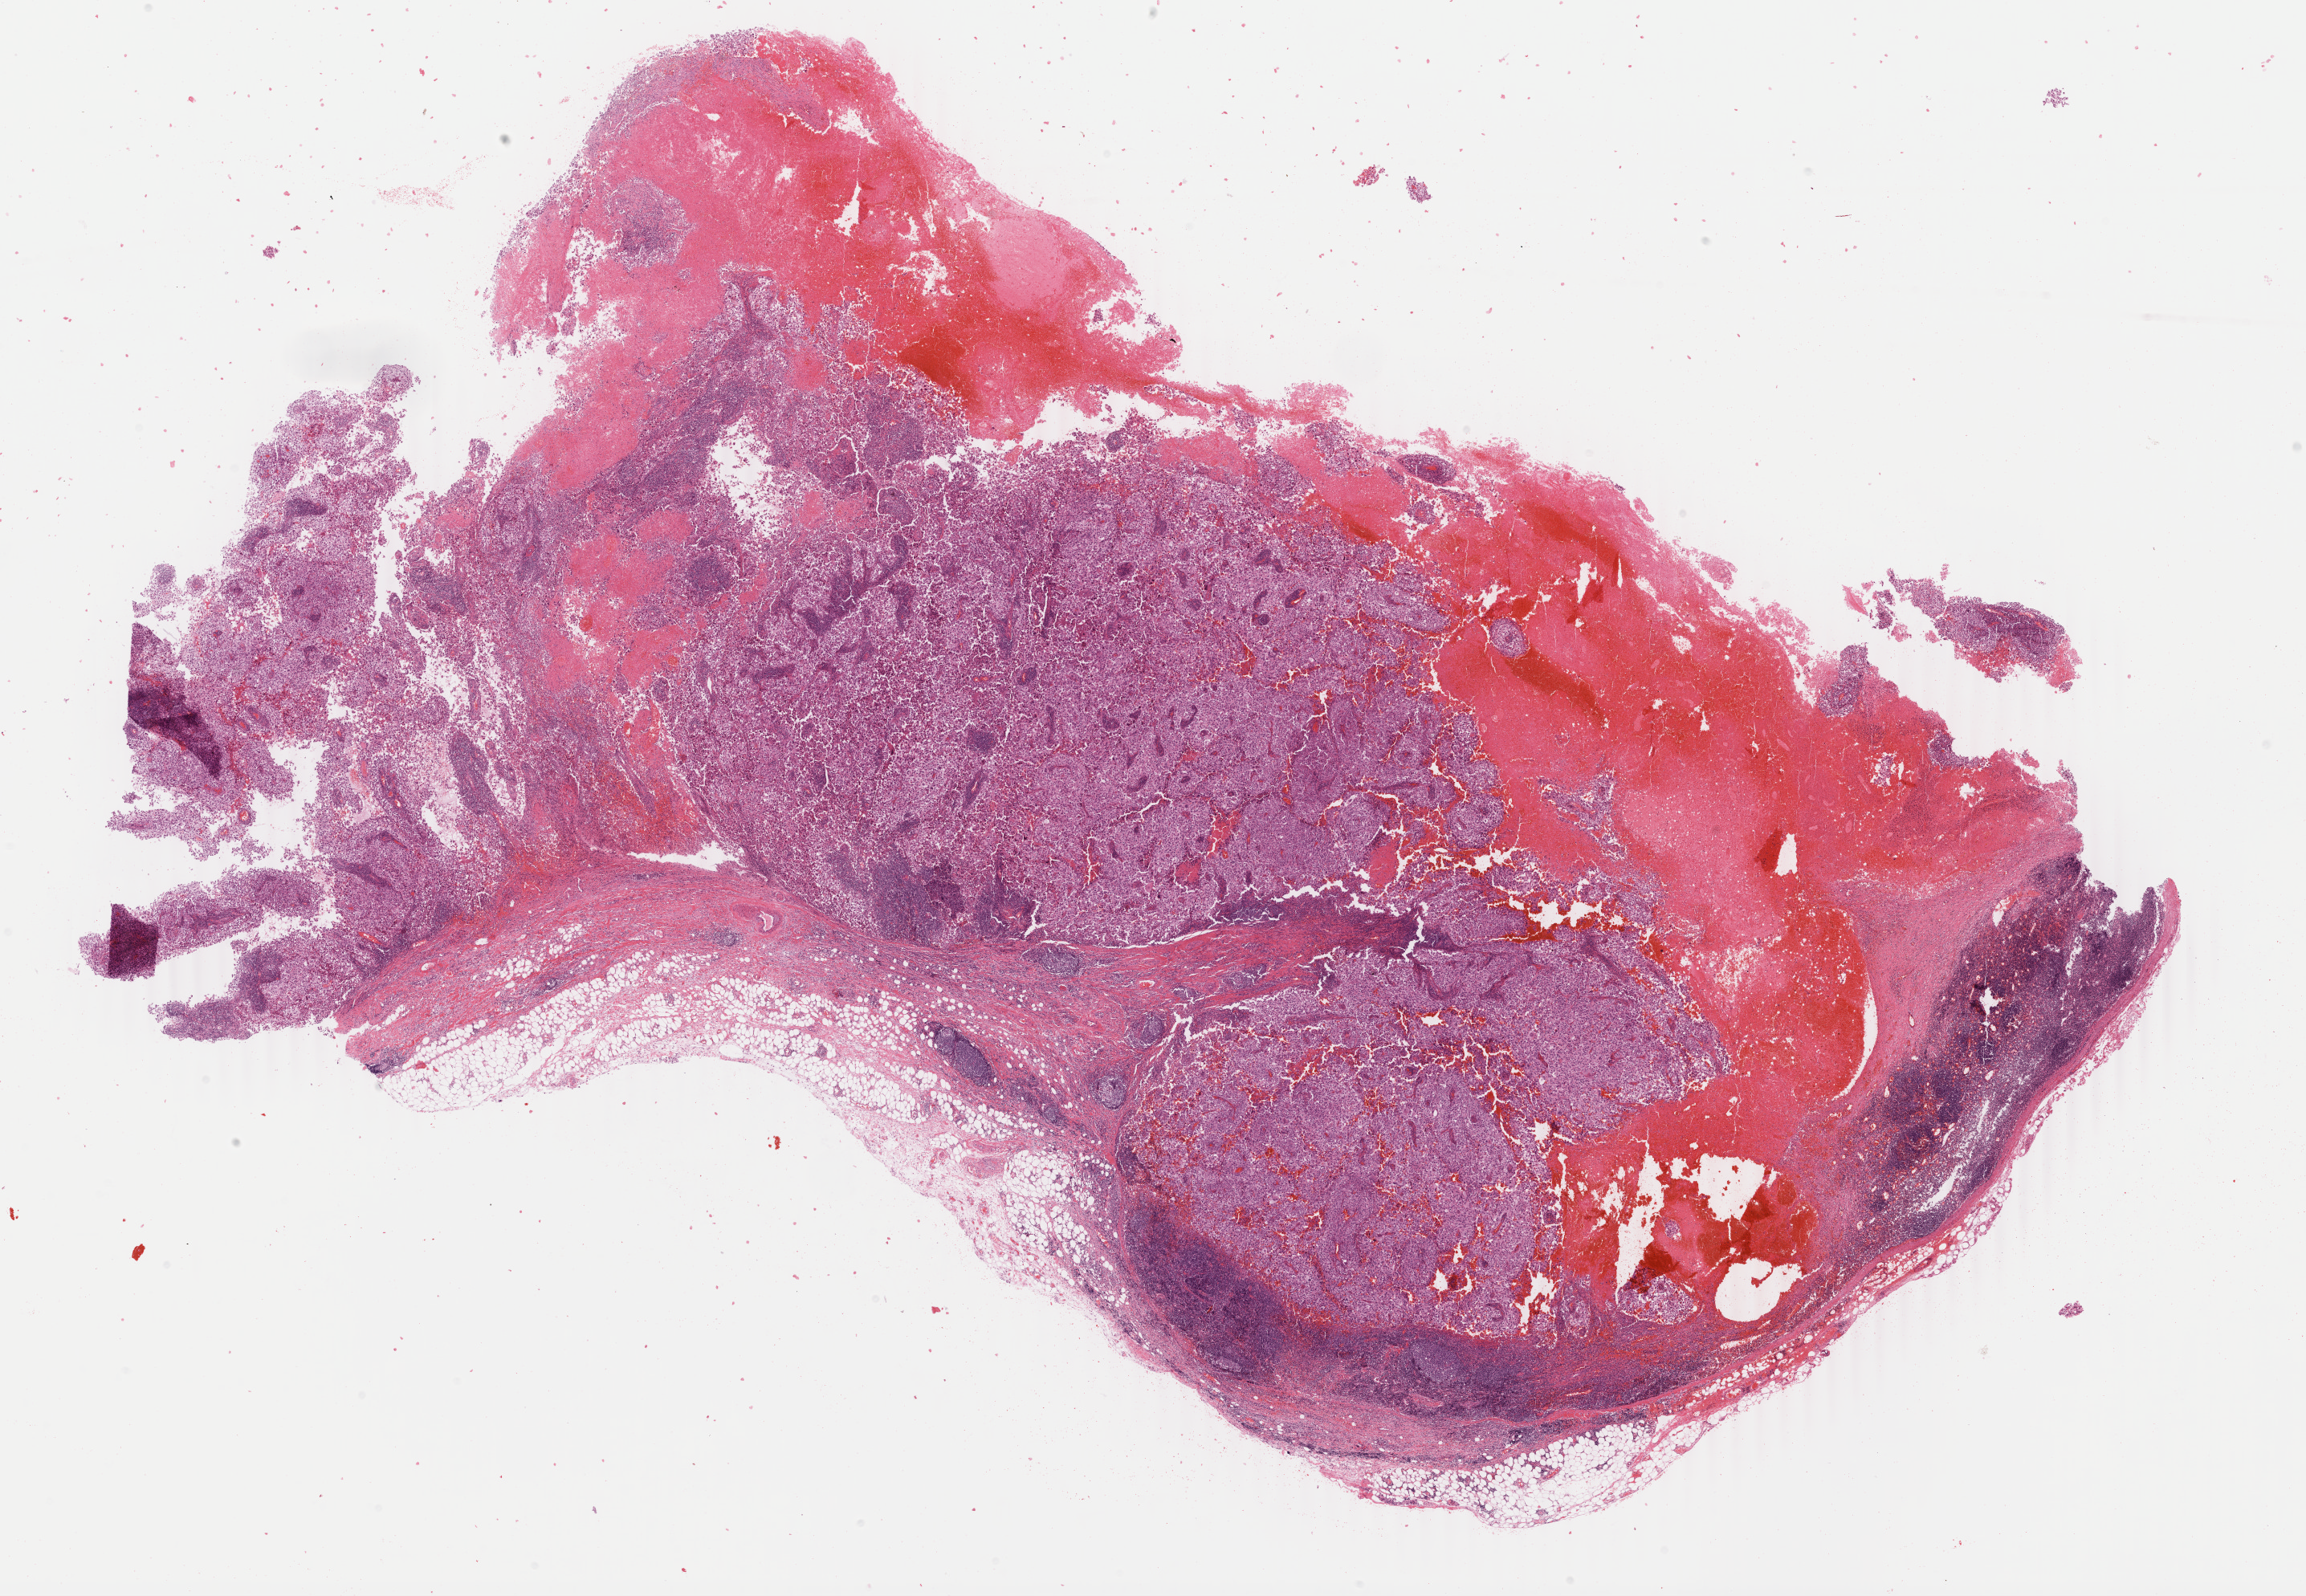
H&E-stained whole-slide image, shown as a low-resolution overview of the whole scanned area (about 22.8 x 15.8 mm, slide scanned at 40x). Formalin-fixed paraffin-embedded (FFPE) diagnostic section. Metastatic tumour sample, sampled site: lymph nodes of axilla or arm. Male, age 71 years at initial diagnosis.
This section: metastatic tumour tissue. Patient diagnosis: Malignant melanoma, NOS.